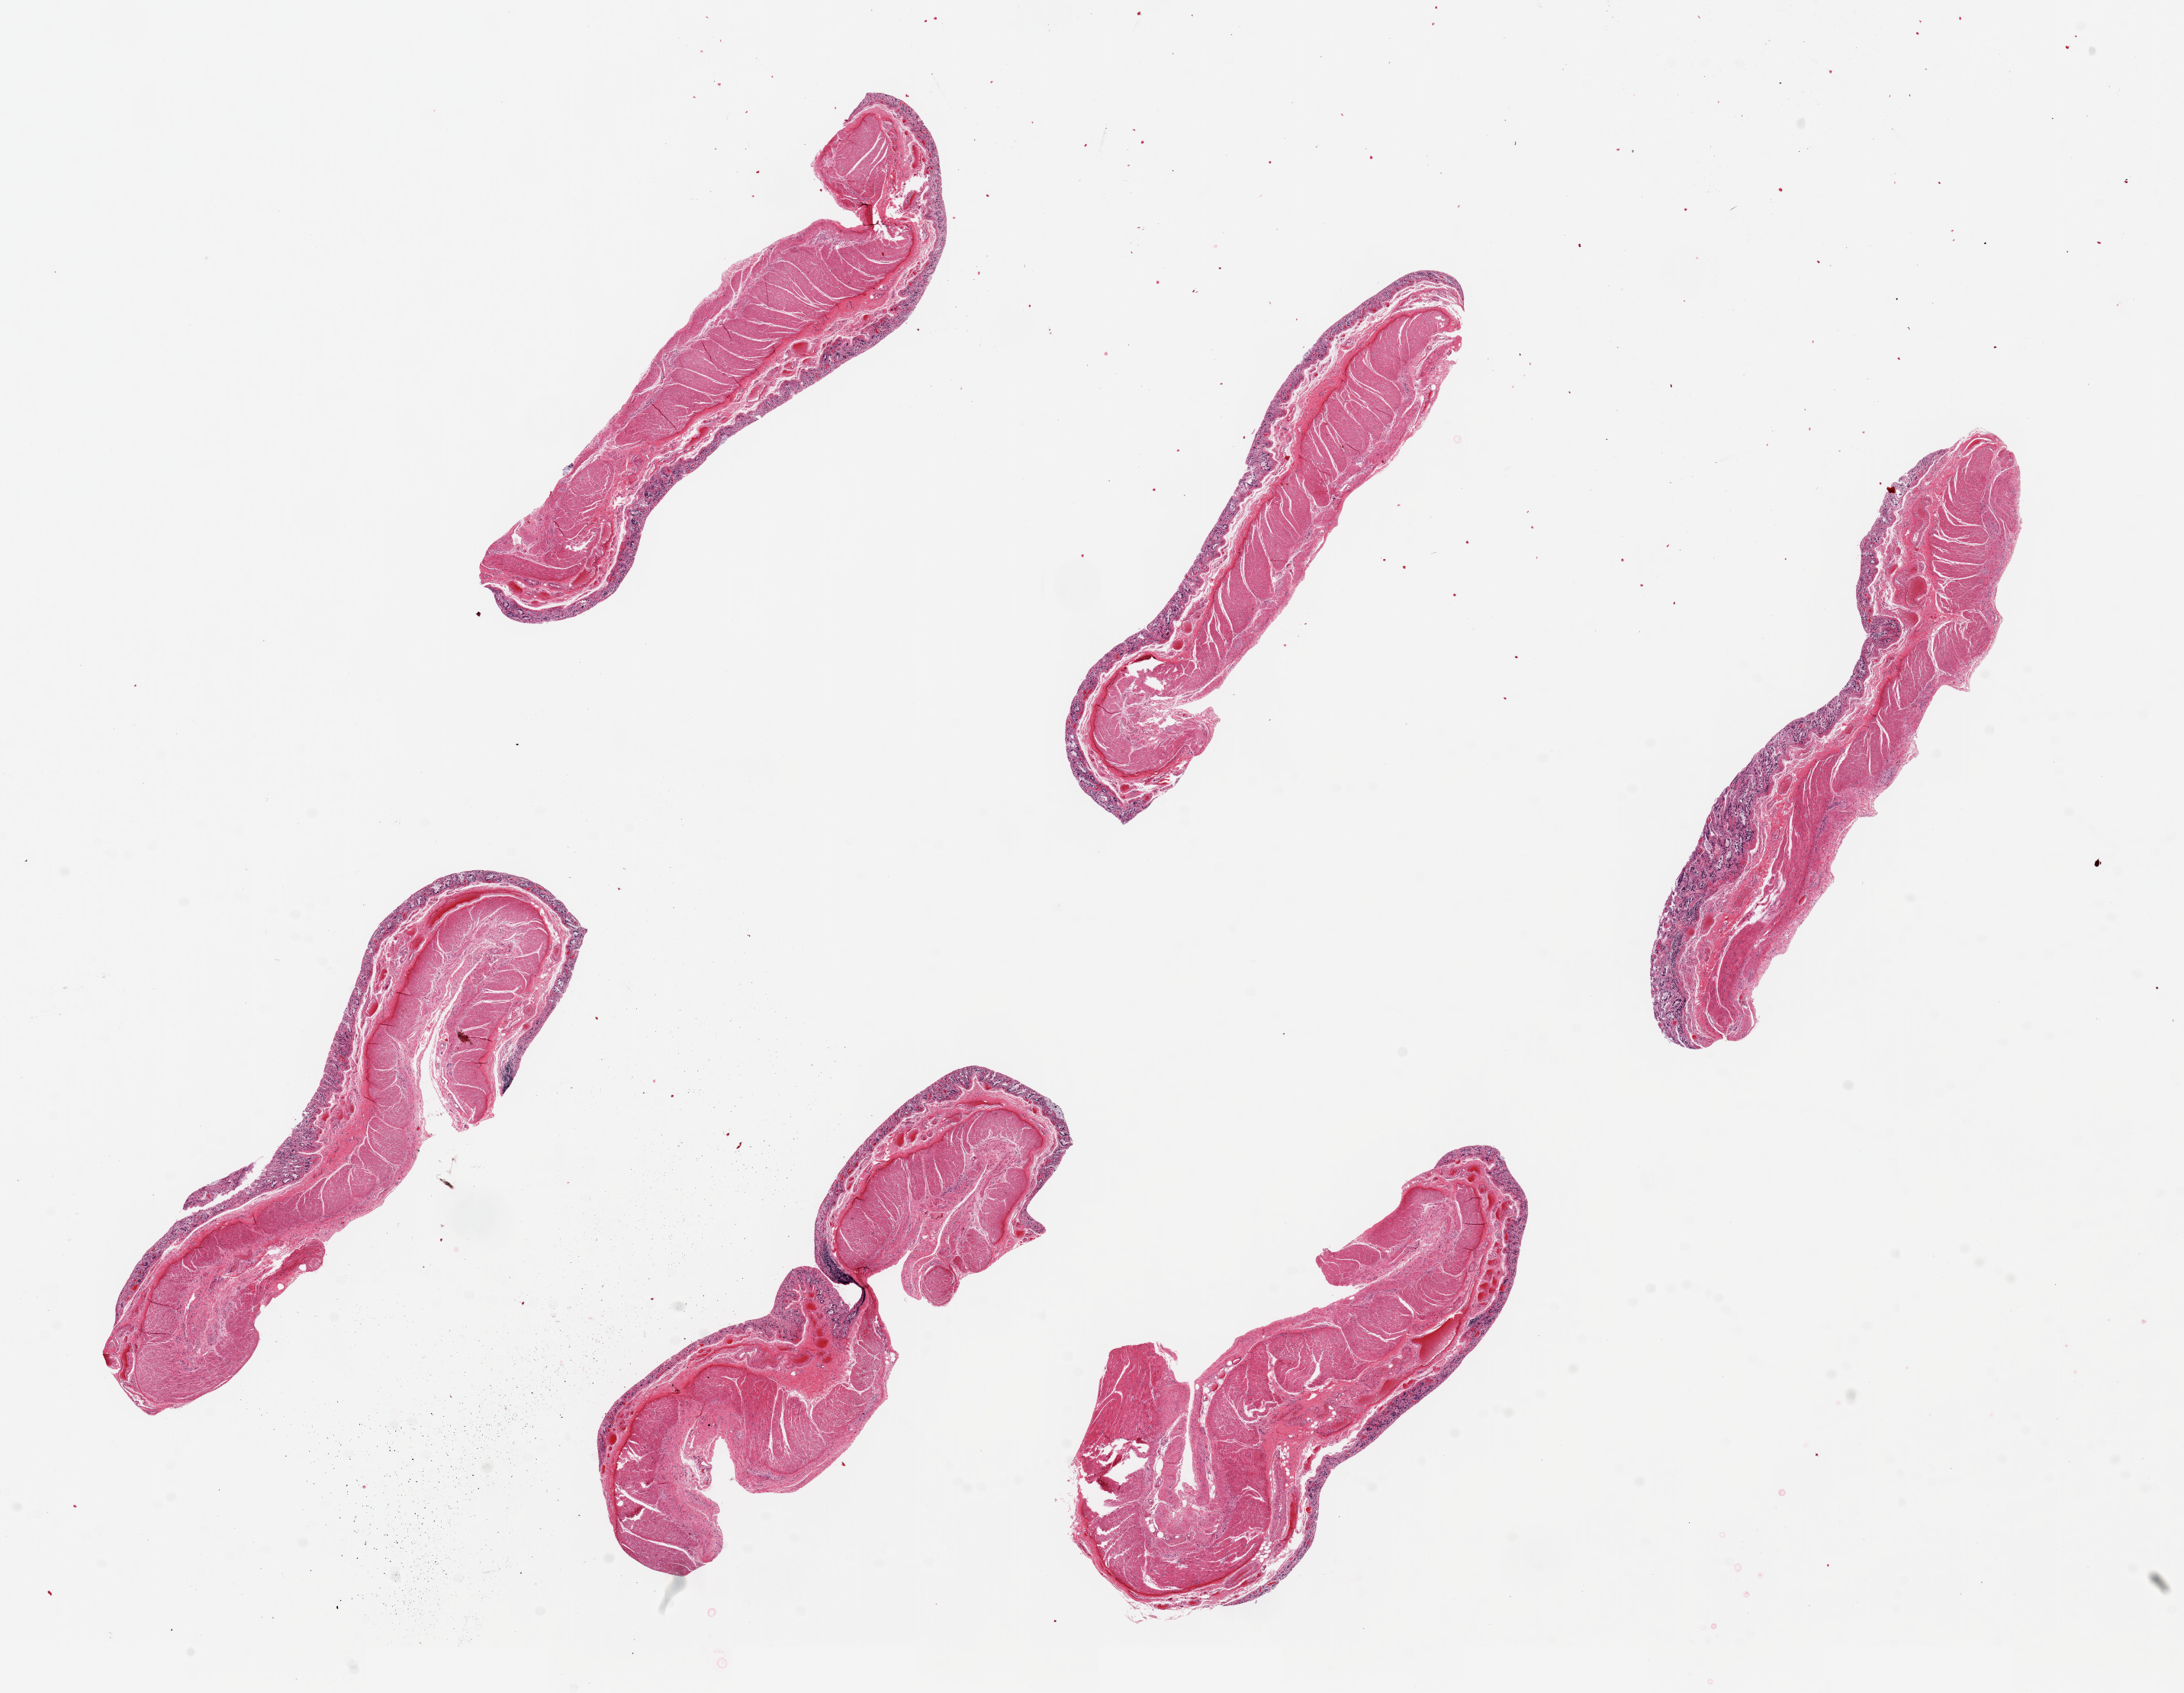
Whole-slide image, hematoxylin and eosin (H&E) stain, a low-resolution overview of the entire scanned area, about 22.6 x 17.6 mm. PAXgene-fixed, paraffin-embedded tissue. Sampled site (target tissue): transverse colon. Tissue donor sample. Male donor.
* reviewer comment on this tissue sample: 6 pieces, up to 7x1.5mm; mucosa = 3, muscle =2 (autolysis)